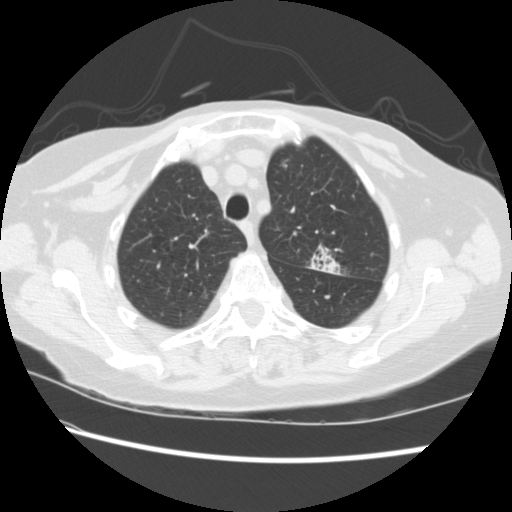
Low-dose screening chest CT, one axial slice; position 173 of 224 along the scan axis; reconstruction kernel STANDARD; lung window (W 1500 / L -600 HU); 2.5 mm slice thickness; 512 × 512 image matrix.
Annotated regions visible in this slice (manually delineated by an expert):
- lesion 1 (tumor, upper lobe of left lung): bounding box (x1, y1, x2, y2) in pixels: (309, 246, 340, 275)